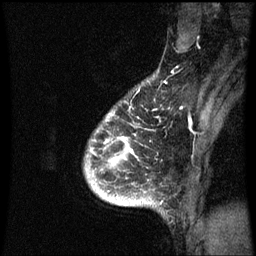
Breast MRI (dynamic contrast-enhanced), one sagittal slice; position 54 of 60 along the scan axis; dynamic contrast-enhanced series, image 2 of 3 at this slice position (ordered by acquisition); 1.5 T; TE 4.2 ms, TR 8.9 ms; 2 mm slice thickness; 256 × 256 image matrix, field of view 200 × 200 mm. Patient: female, 35 years. Case-level facts recorded for this patient, not image findings: setting: breast cancer imaged before/during neoadjuvant chemotherapy; receptor status: HR-positive, HER2-negative.
Outlined on this slice (semi-automatically segmented with operator editing):
- analysis volume of interest (the breast-tissue region the enhancement analysis was run in; not a lesion): bounding box <87,114,153,205> (left, top, right, bottom; pixels)
- tumour enhancement mask (voxels above the 70 % enhancement threshold inside the analysis volume of interest): <91,138,133,205>